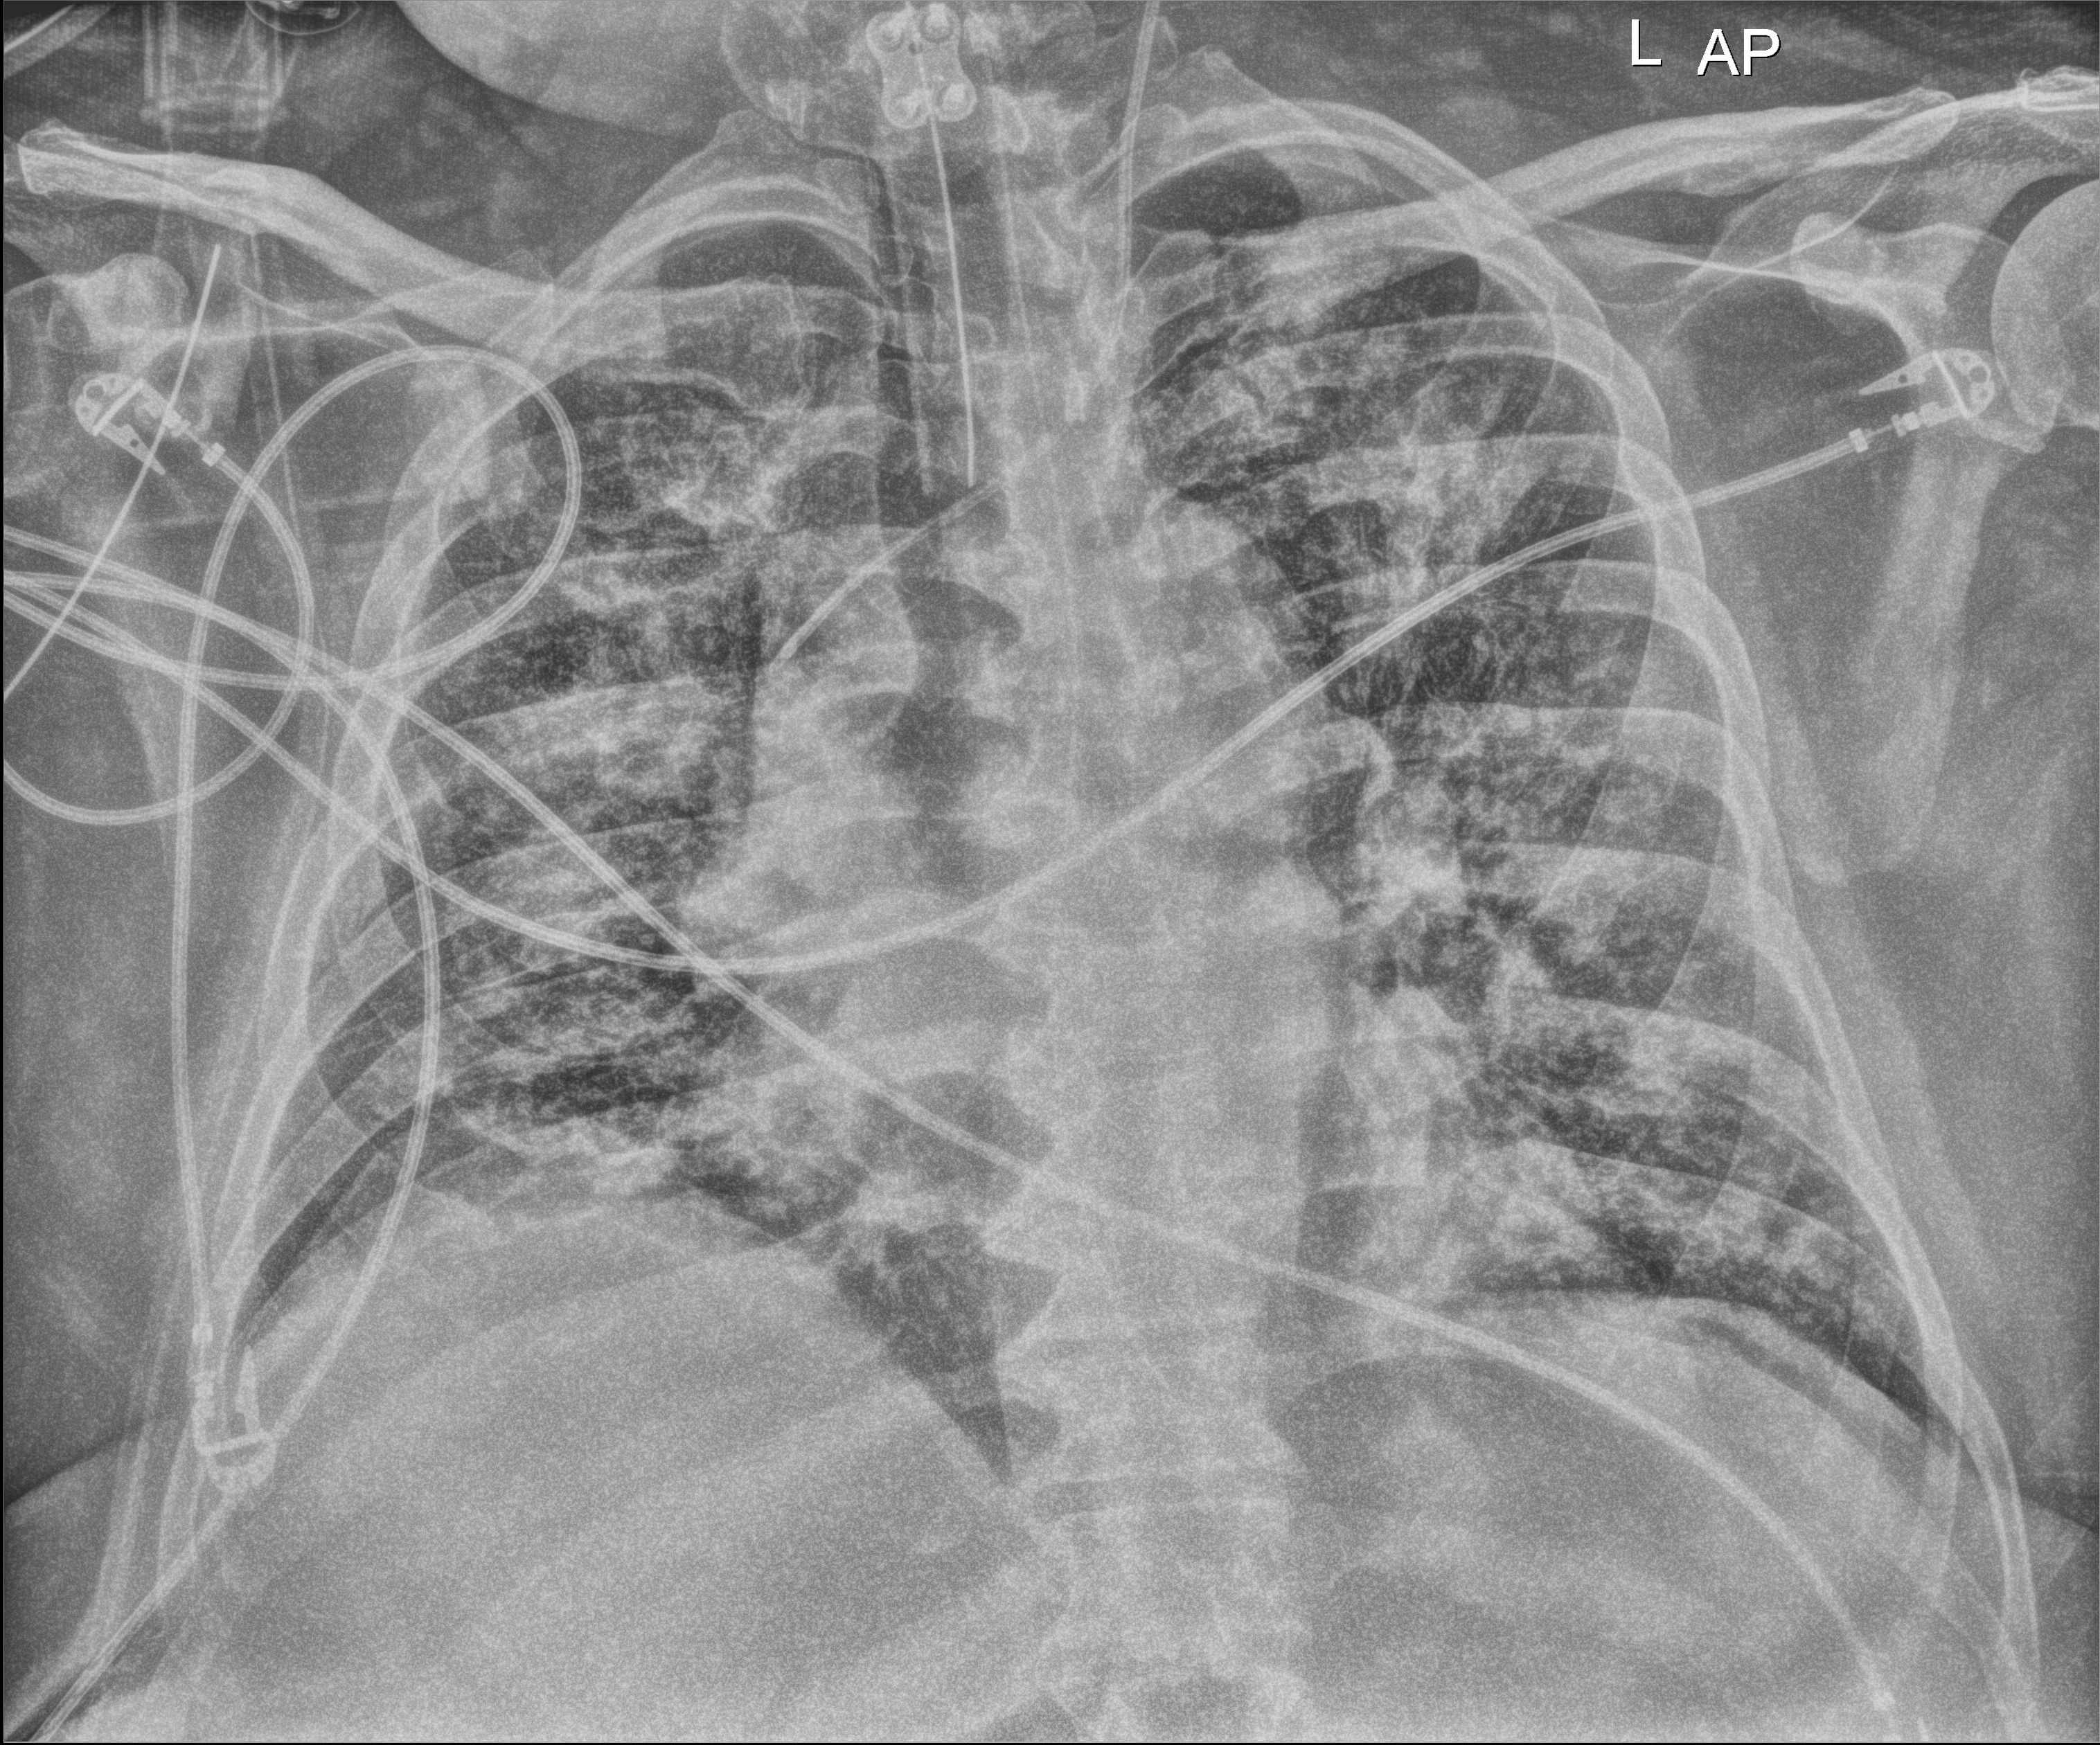
Portable chest radiograph, anteroposterior (AP) projection. Patient hospitalised with COVID-19; male, aged 18–59 years.
From the hospital-stay record, not from the radiograph (when in the stay this image was taken is not recorded):
- COPD (admission record): no
- smoking status (admission record): never
- admitted to intensive care during this hospital stay: yes